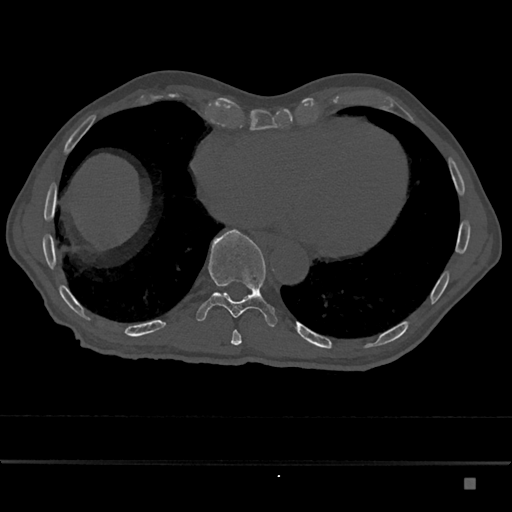
CT including the spine, one axial slice; slice 745 of 797 in the series (ordered by position); reconstruction kernel Br40s/3; 120 kVp; bone window (W 1800 / L 400 HU); 0.5 mm slice thickness; 512 × 512 image matrix, field of view 390 × 390 mm. Male patient, age 72 years. Case-level facts recorded for this patient, not image findings: primary cancer: prostate.
Outlined on this slice (semi-automatic segmentation, software-assisted and operator-edited):
- T10 vertebra: bounding box <196,229,277,327> (left, top, right, bottom; pixels)
- T9 vertebra: <231,330,242,346>